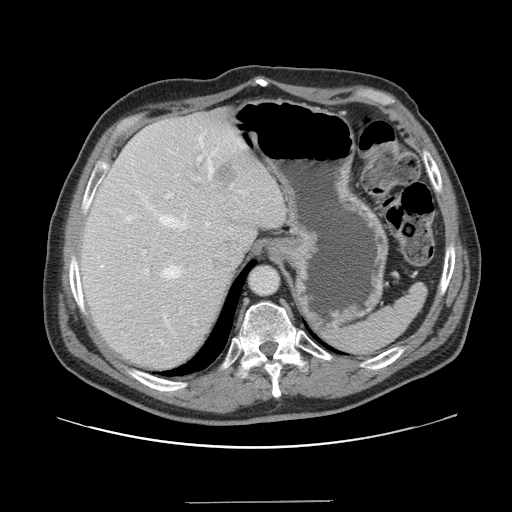
Contrast-enhanced abdominal CT, one axial slice. Slice 117 of 151 in the series (ordered by position). Soft-tissue window (W 400 / L 40 HU). 2.5 mm slice thickness. 512 × 512 image matrix. Male patient, age 63 years. From the clinical record (not read from this slice): diagnosis: colorectal cancer liver metastases, imaged before liver resection; multiple liver metastases: no; largest metastasis: 2.1 cm; disease in both lobes: no.
Structures marked on this image (manually delineated by an expert):
- hepatic veins: bounding box (x1, y1, x2, y2) in pixels: (100, 136, 216, 279)
- liver: (79, 110, 286, 371)
- planned liver remnant (the part of the liver to remain after resection): (80, 117, 259, 371)
- portal vein (with intrahepatic branches): (142, 155, 232, 274)
- liver metastasis: (215, 159, 236, 186)